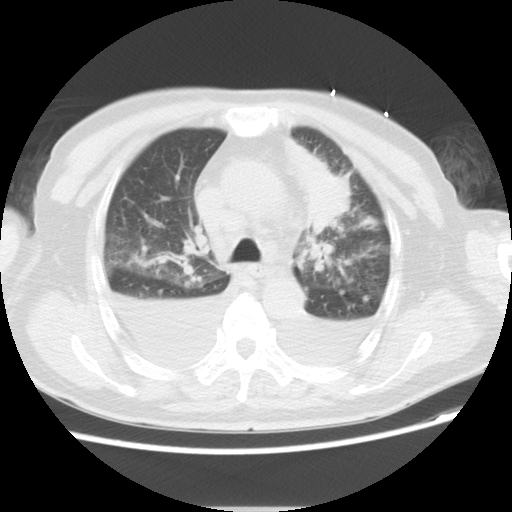
Chest CT, one axial slice; slice 17 of 21 in the series (ordered by position); lung window (W 1500 / L -600 HU); 5 mm slice thickness; 512 × 512 image matrix. Patient: male, 66 years. Case-level facts recorded for this patient, not image findings: clinical TNM (as recorded): T1c N0 M0.
Annotated regions visible in this slice (bounding box drawn by a radiologist):
- lung tumour (recorded histology: adenocarcinoma): bounding box <279,135,356,238> (left, top, right, bottom; pixels)